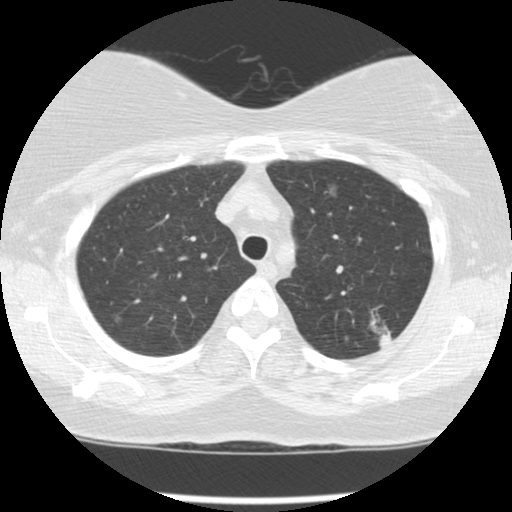
Low-dose screening chest CT, one axial slice; position 104 of 127 along the scan axis; reconstruction kernel STANDARD; 120 kVp; lung window (W 1500 / L -600 HU); 2.5 mm slice thickness; 512 × 512 image matrix, field of view 310 × 310 mm.
Structures marked on this image (outlined manually by an expert reader):
- lesion 1 (tumor, upper lobe of left lung): box from (x=368, y=311) to (x=393, y=348) px